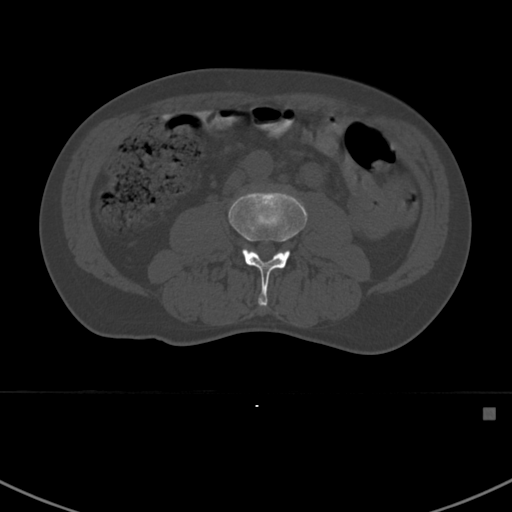
CT including the spine, one axial slice. Position 260 of 412 along the scan axis. 120 kVp. Bone window (W 1800 / L 400 HU). 1.5 mm slice thickness. 512 × 512 image matrix, field of view 358 × 358 mm. Male patient, age 59 years. From the clinical record (not read from this slice): primary cancer: prostate.
Annotated regions visible in this slice (semi-automatic segmentation, software-assisted and operator-edited):
- L3 vertebra: bounding box (x1, y1, x2, y2) in pixels: (228, 190, 307, 307)